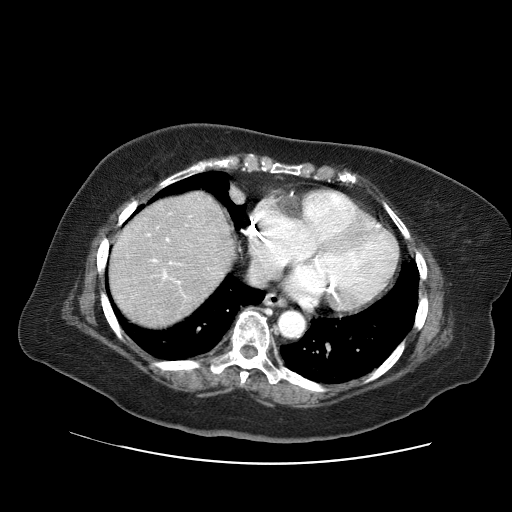
Contrast-enhanced abdominal CT (liver protocol), one axial slice. Reconstruction kernel STANDARD. 120 kVp. Soft-tissue window (W 400 / L 40 HU). 2.5 mm slice thickness. 512 × 512 image matrix, field of view 400 × 400 mm. Case-level facts recorded for this patient, not image findings: diagnosis: hepatocellular carcinoma (patient treated with transarterial chemoembolisation; whether this scan precedes or follows treatment is not stated here); TNM stage (as recorded): Stage-II; Child-Pugh class: A; tumour nodularity: multinodular.
Outlined on this slice (semi-automatic segmentation, software-assisted and operator-edited):
- abdominal aorta: box from (x=278, y=311) to (x=304, y=337) px
- liver parenchyma outside the tumour (the mass and vessels are separate outlines, so this box may not span the whole liver): (x=110, y=191)–(x=234, y=326)
- liver vessels: (x=147, y=224)–(x=188, y=284)